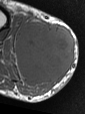
MRI of an extremity soft-tissue mass, one axial slice. Position 24 of 47 along the scan axis. MR volume resampled by the dataset authors to the PET/CT grid (not the native acquisition matrix). 85 × 114 image matrix, field of view 83 × 111 mm. Male patient. From the clinical record (not read from this slice): histological type: pleiomorphic liposarcoma; grade: high; site of the primary tumour: right calf.
Annotated regions visible in this slice (expert contour drawn on MRI and transferred to this co-registered scan by the dataset authors):
- gross tumour volume including surrounding oedema: bounding box [x1, y1, x2, y2] px = [15, 16, 75, 90]
- gross tumour volume (mass): [15, 21, 75, 83]